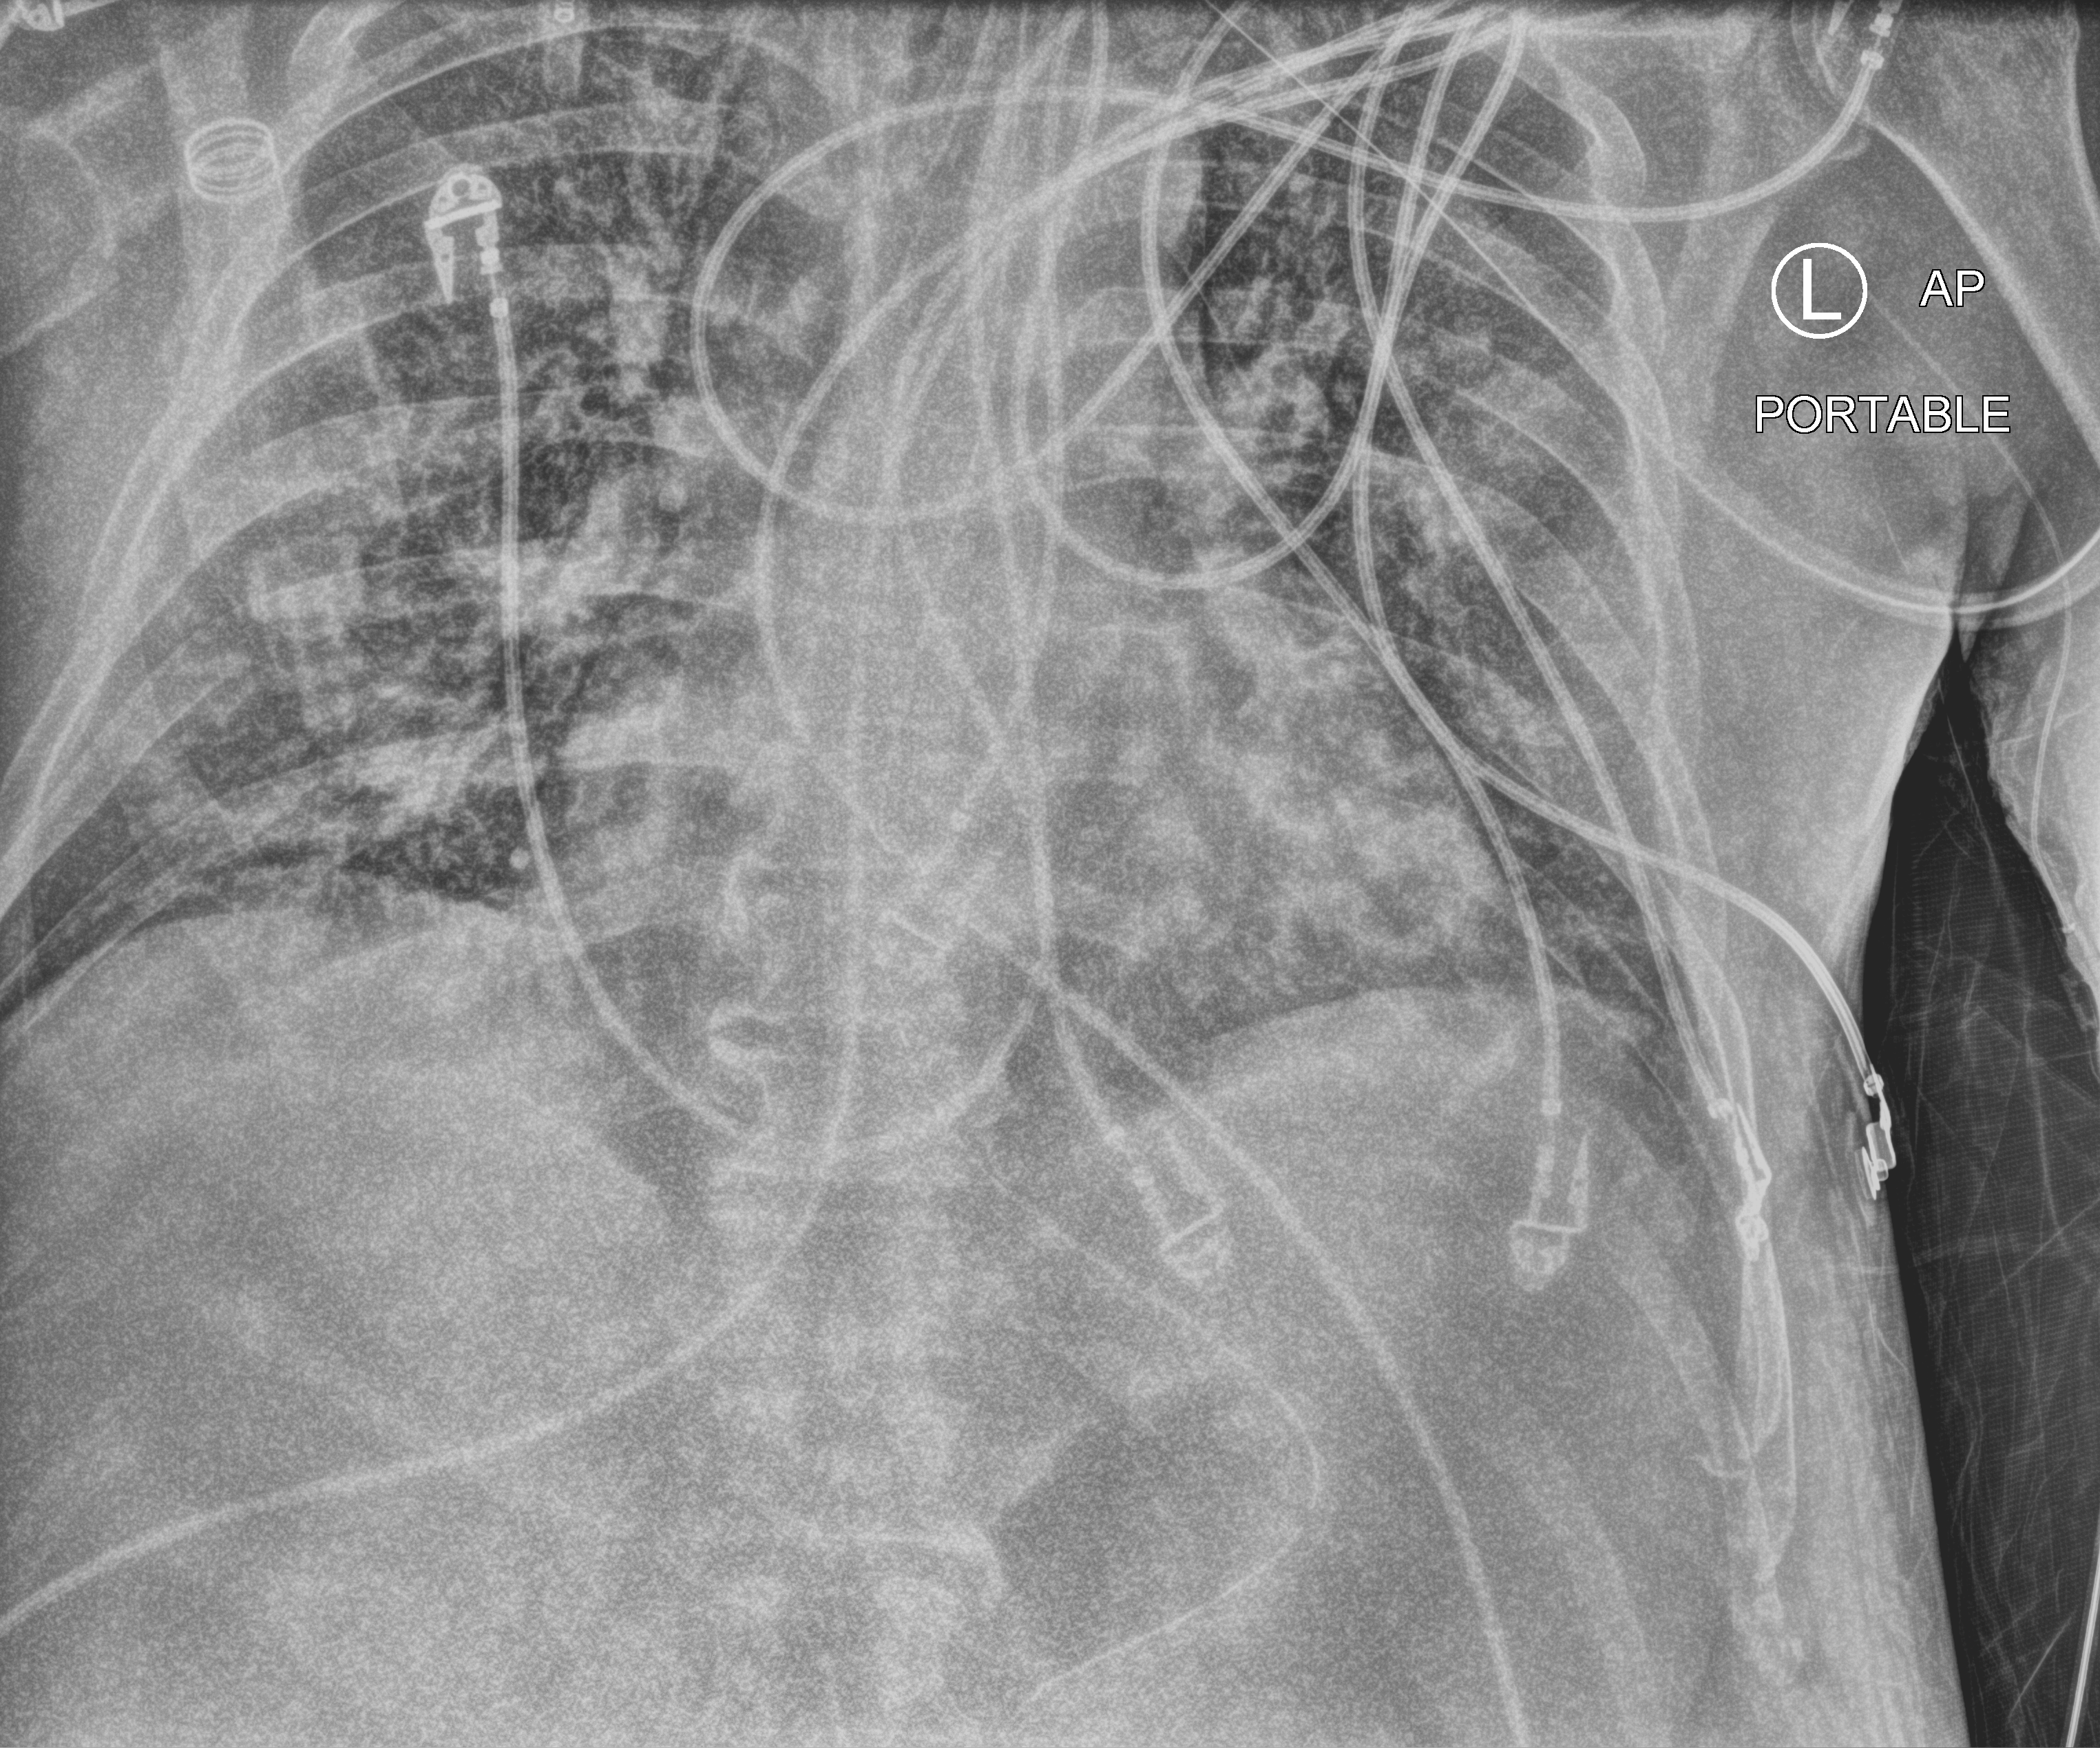
Portable chest radiograph, anteroposterior (AP) projection. Patient hospitalised with COVID-19; male, aged 18–59 years.
From the hospital-stay record, not from the radiograph (when in the stay this image was taken is not recorded):
- other chronic lung disease (admission record): no
- admitted to intensive care during this hospital stay: no
- hypertension (admission record): no